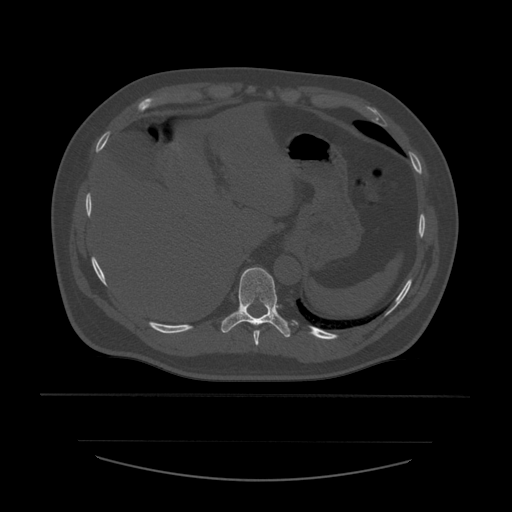
CT including the spine, one axial slice; position 300 of 532 along the scan axis; 120 kVp; bone window (W 1800 / L 400 HU); 1.25 mm slice thickness; 512 × 512 image matrix, field of view 441 × 441 mm. Patient age 44 years. Case-level facts recorded for this patient, not image findings: primary cancer: soft tissue sarcoma.
Structures marked on this image (semi-automatic segmentation, software-assisted and operator-edited):
- T10 vertebra: bounding box [x1, y1, x2, y2] px = [221, 268, 294, 338]
- T9 vertebra: [253, 330, 261, 346]